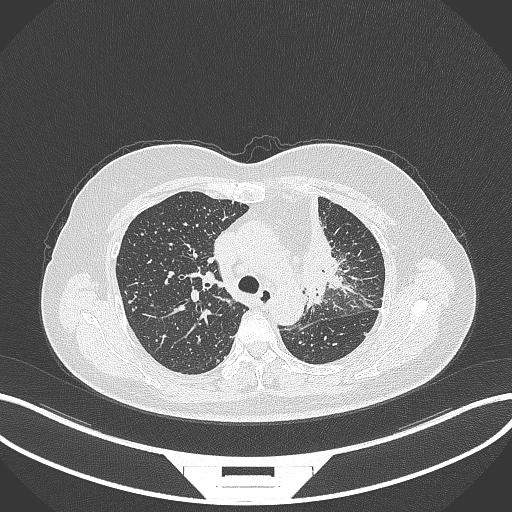
Chest CT, one axial slice. Reconstruction kernel B70f. 120 kVp. Lung window (W 1500 / L -600 HU). 512 × 512 image matrix. Female patient, age 49 years. From the clinical record (not read from this slice): clinical TNM (as recorded): T1c N0 M1.
Structures marked on this image (bounding box drawn by a radiologist):
- lung tumour (recorded histology: adenocarcinoma): bounding box (x1, y1, x2, y2) in pixels: (288, 187, 349, 307)